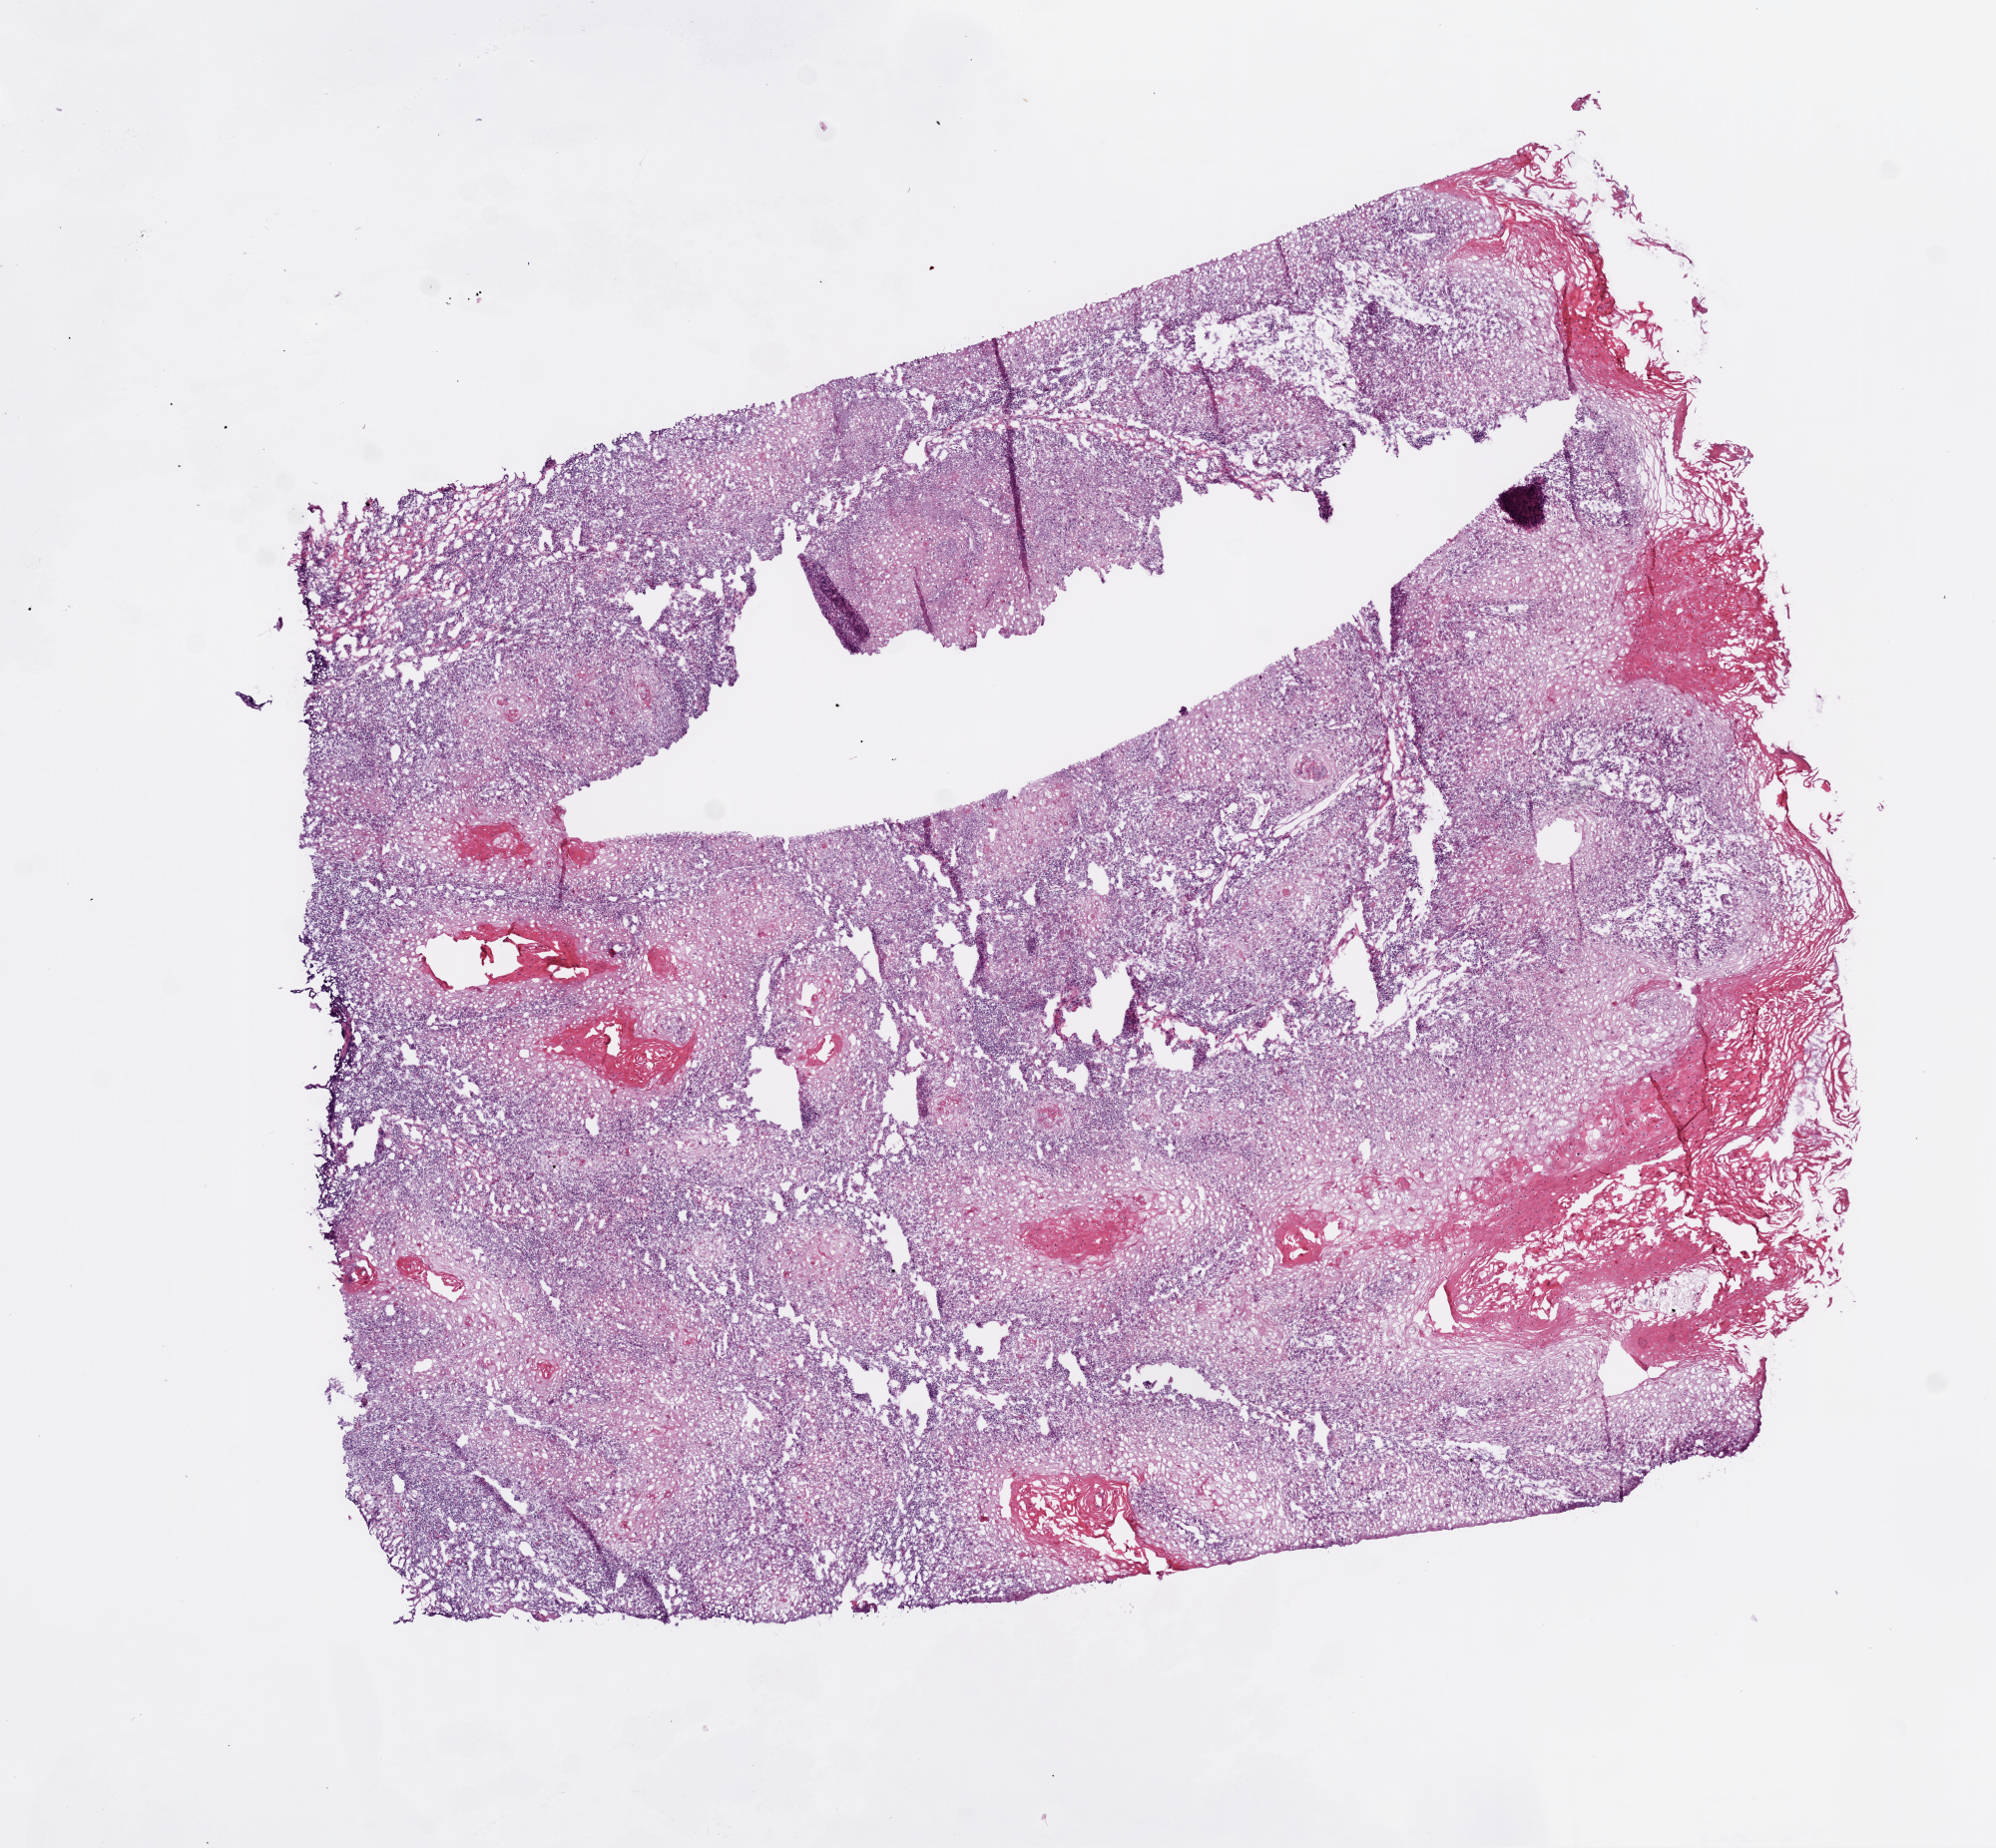
Digitized H&E tissue section (whole slide), low-resolution overview of the scanned area, about 8.0 x 7.4 mm (acquisition: 20x scan). Frozen section from the bottom of the tissue portion. Sample: primary tumour, head and neck. Female, age 73 years at initial diagnosis. Histologic grade: G2 (moderately differentiated). Slide review estimates, as recorded: tumour cells 95%, tumour nuclei 70%, normal cells 0%, stromal cells 5%, necrosis 0%. Infiltration values recorded for this section: lymphocyte infiltration 25%, monocyte infiltration 0%, neutrophil infiltration 0%.
Diagnosis: Squamous cell carcinoma, NOS (overlapping lesion of lip, oral cavity and pharynx). Laterality: right.